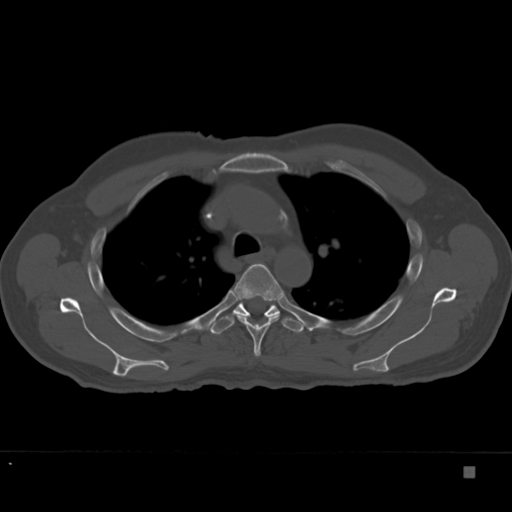
CT including the spine, one axial slice. Slice 265 of 332 in the series (ordered by position). Reconstruction kernel Br40s. Bone window (W 1800 / L 400 HU). 1.5 mm slice thickness. 512 × 512 image matrix. Male patient, age 72 years. From the clinical record (not read from this slice): primary cancer: skeletal.
Structures marked on this image (semi-automatic segmentation, software-assisted and operator-edited):
- T4 vertebra: bounding box (x1, y1, x2, y2) in pixels: (232, 263, 284, 357)
- T5 vertebra: (210, 301, 304, 335)